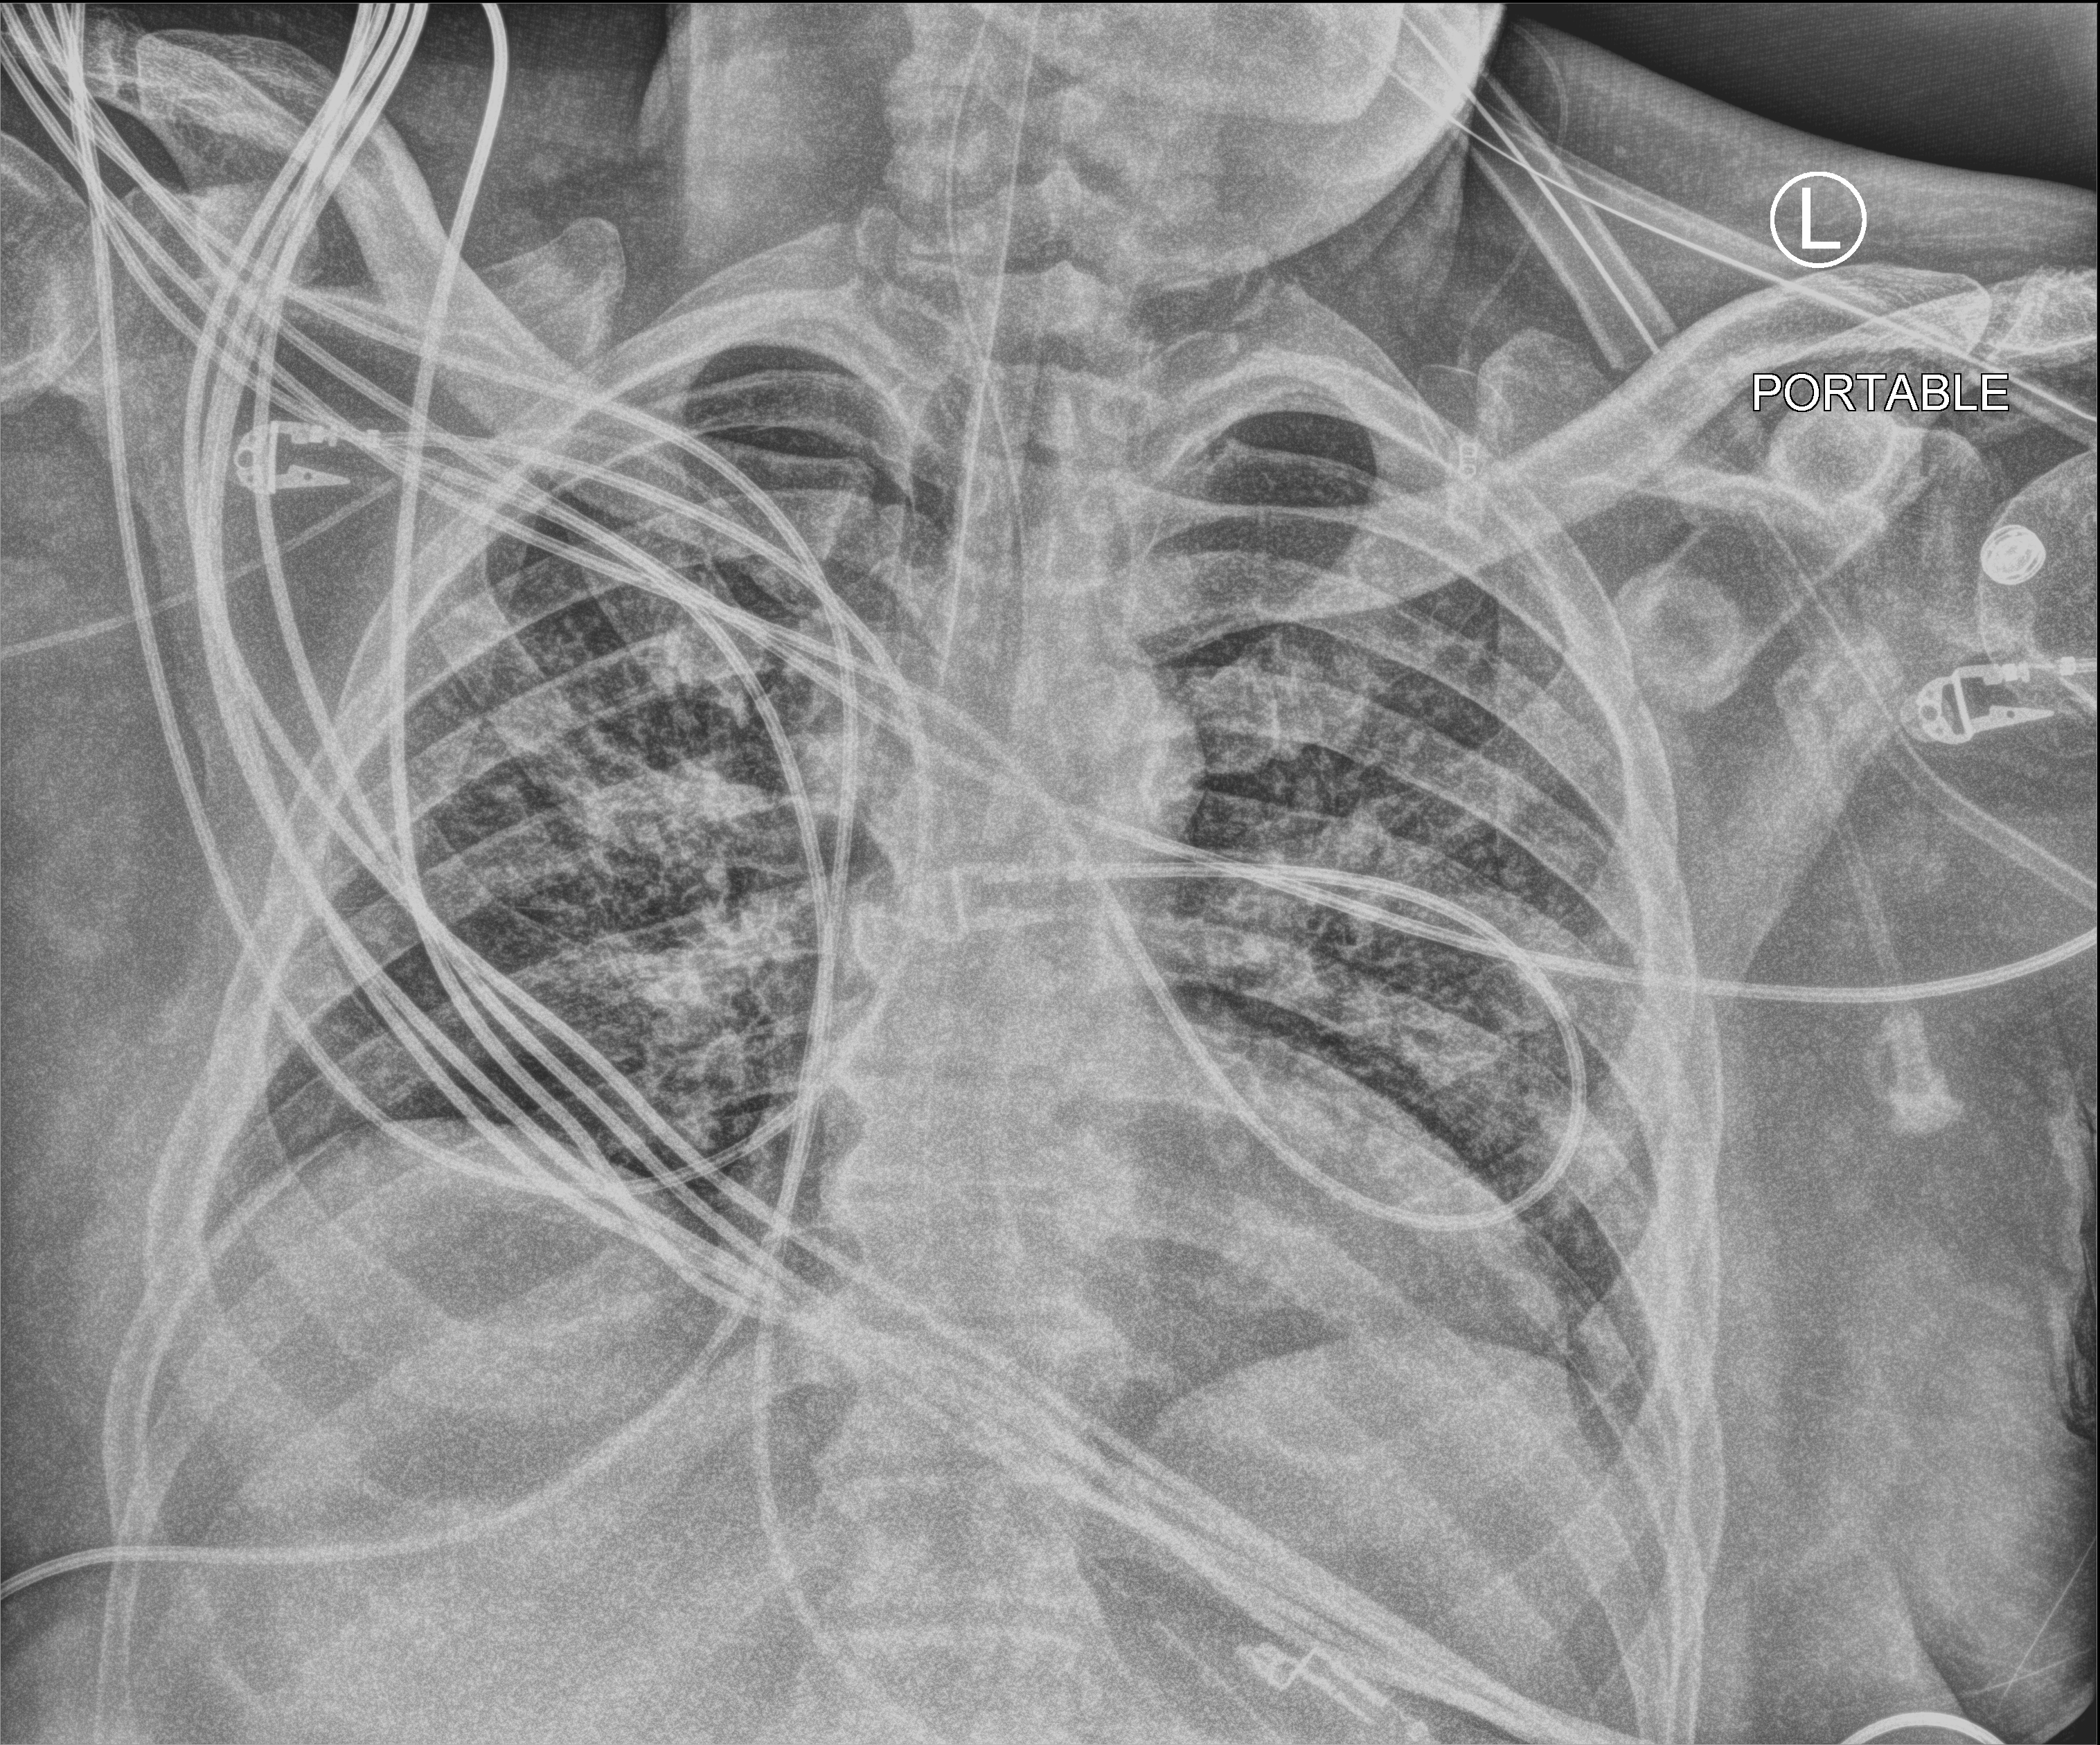
Chest X-ray (portable); anteroposterior (AP) projection. Male patient hospitalised with COVID-19, age 18–59 years.
From the hospital-stay record, not from the radiograph (when in the stay this image was taken is not recorded):
- other chronic lung disease (admission record): no
- smoking status (admission record): never
- chronic kidney disease (admission record): no